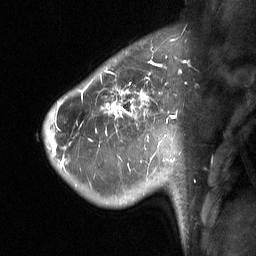
Breast MRI (dynamic contrast-enhanced), one sagittal slice; slice 51 of 64 in the series (ordered by position); dynamic contrast-enhanced study with each time point stored as its own series, time point 2 of 3 at this slice position (early post-contrast, ordered by acquisition time); 1.5 T; TE 4.8 ms, TR 27 ms; 256 × 256 image matrix. Female patient, age 42 years. Case-level facts recorded for this patient, not image findings: setting: breast cancer imaged before/during neoadjuvant chemotherapy; receptor status: triple-negative.
Structures marked on this image (semi-automatic segmentation, software-assisted and operator-edited):
- analysis volume of interest (the breast-tissue region the enhancement analysis was run in; not a lesion): bounding box <49,45,196,197> (left, top, right, bottom; pixels)
- tumour enhancement mask (voxels above the 90 % enhancement threshold inside the analysis volume of interest): <52,62,176,151>